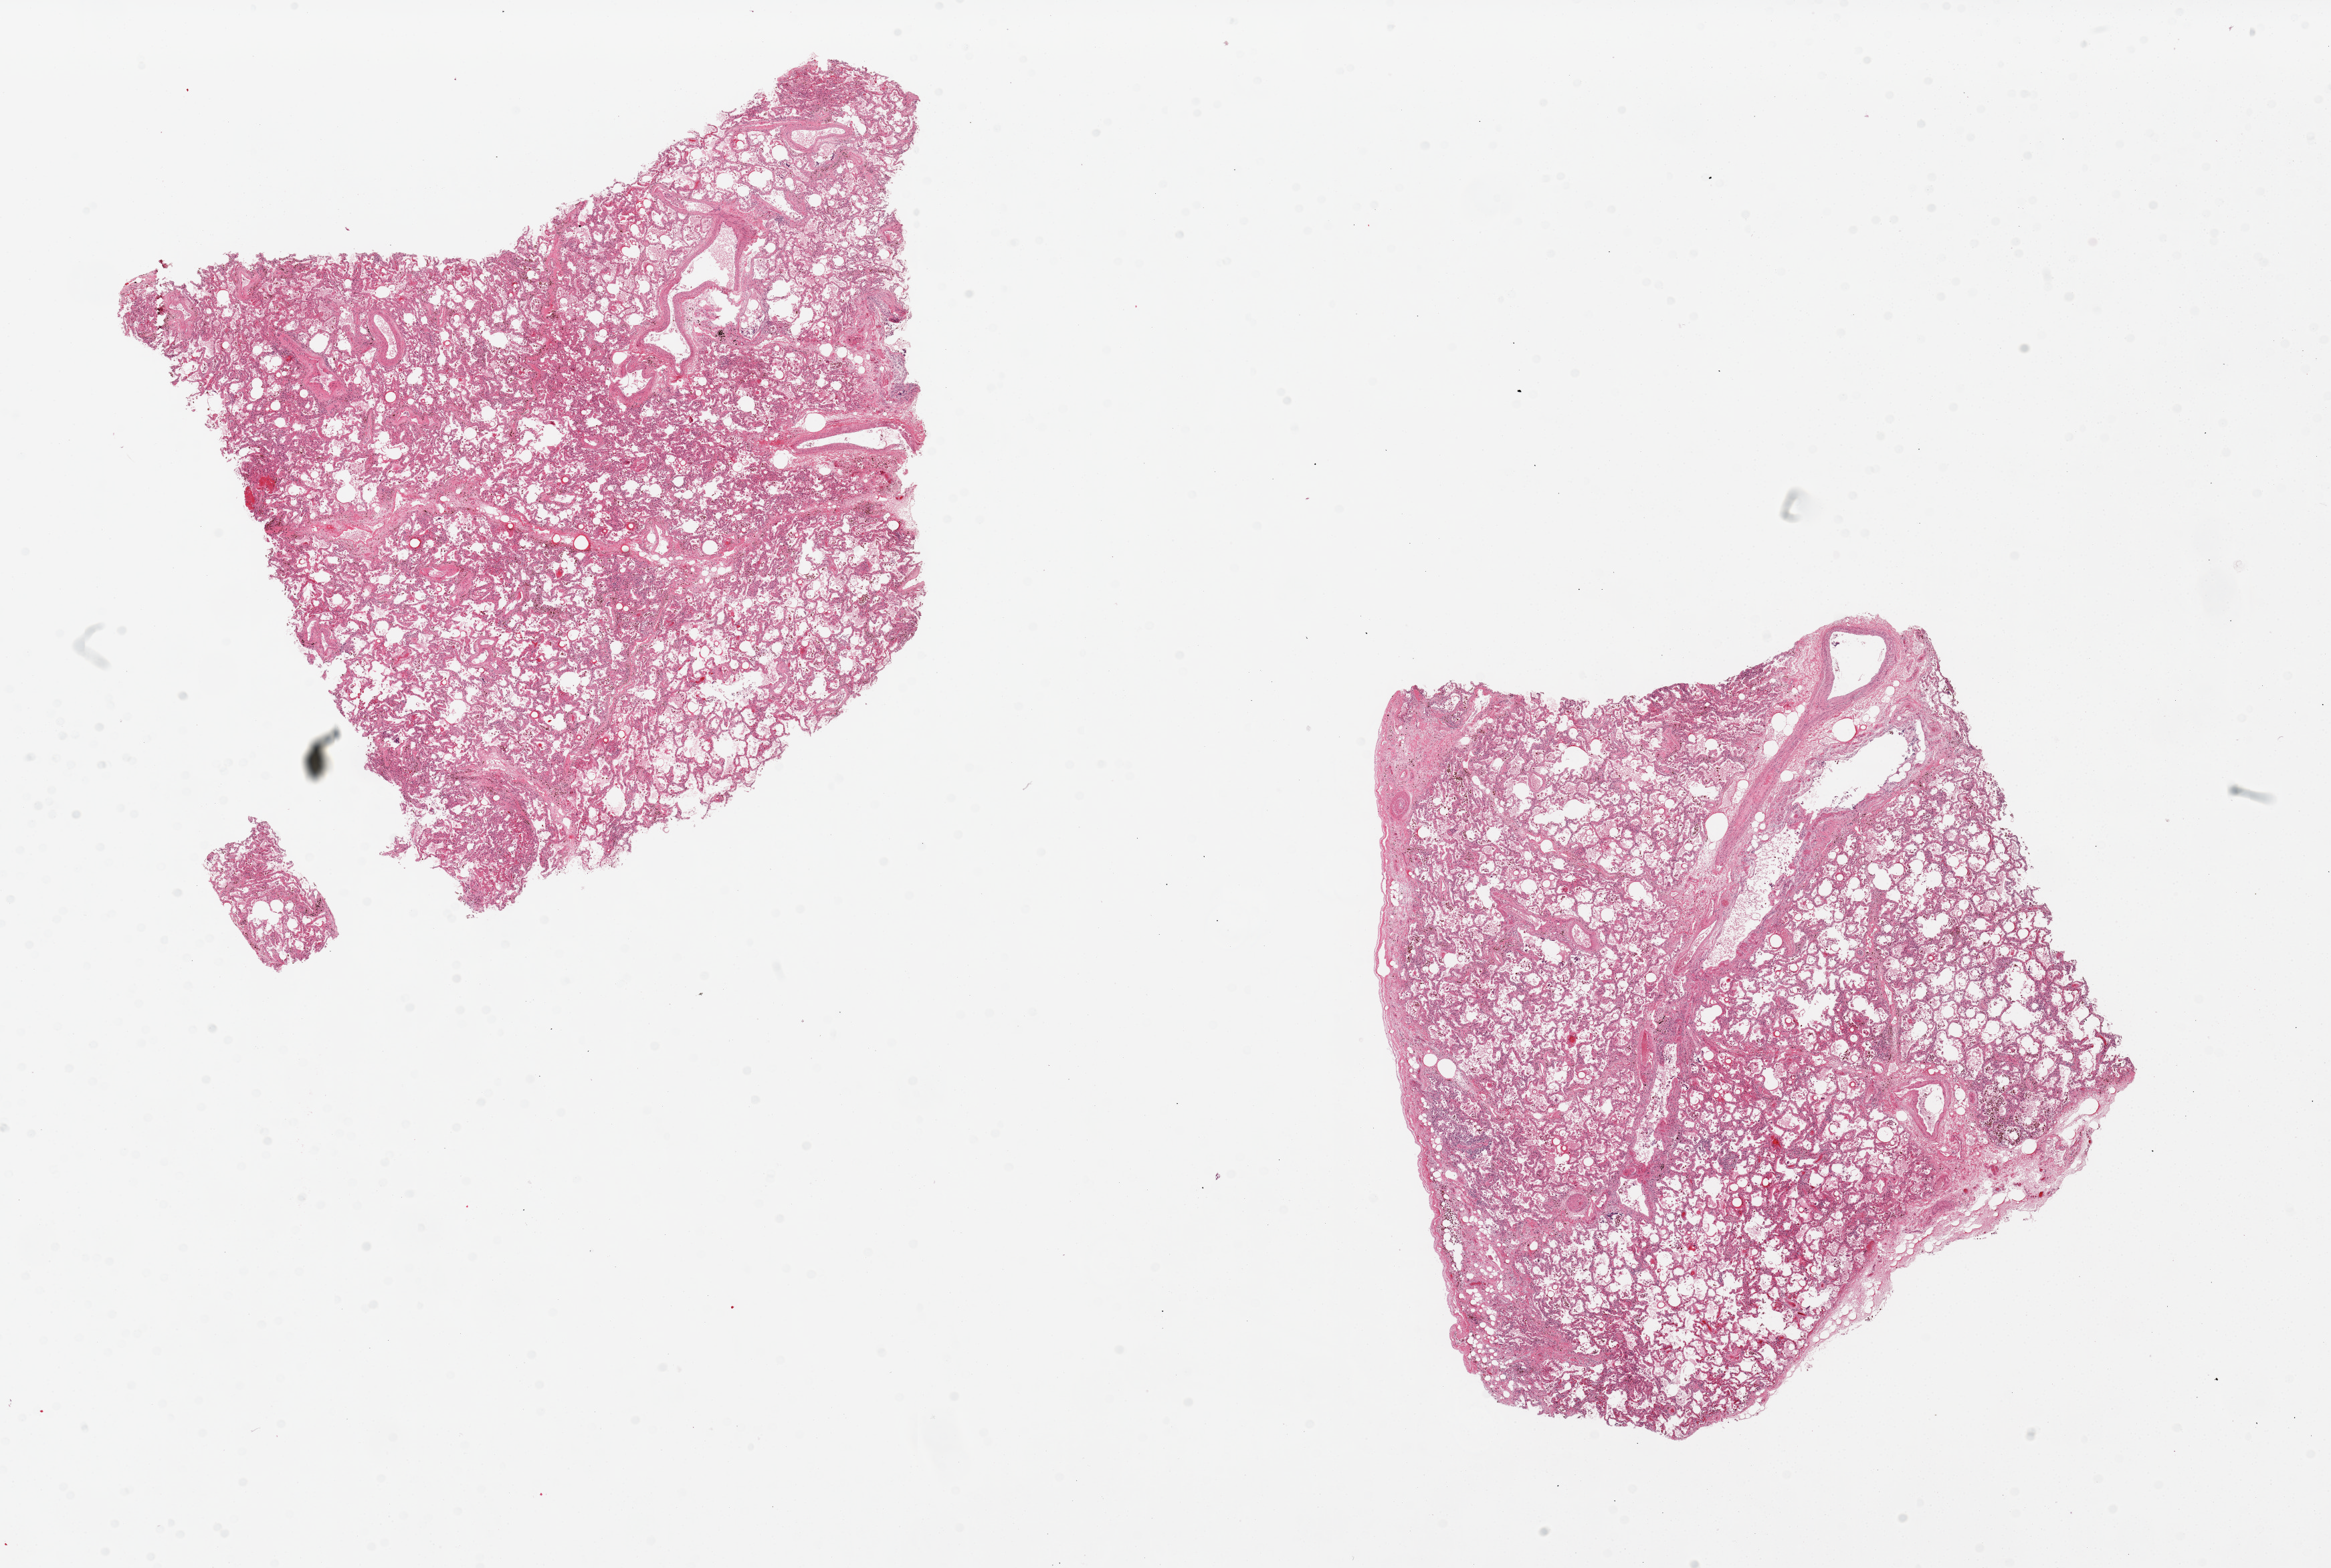
Whole-slide image, H&E stain, brightfield, a low-resolution overview of the entire scanned area, about 27.6 x 18.5 mm, PAXgene-fixed, paraffin-embedded tissue, target tissue: lung, tissue donor sample. Donor sex: male.
• review note (as recorded): 2 pieces; numerous hemosiderin-laden macrophages